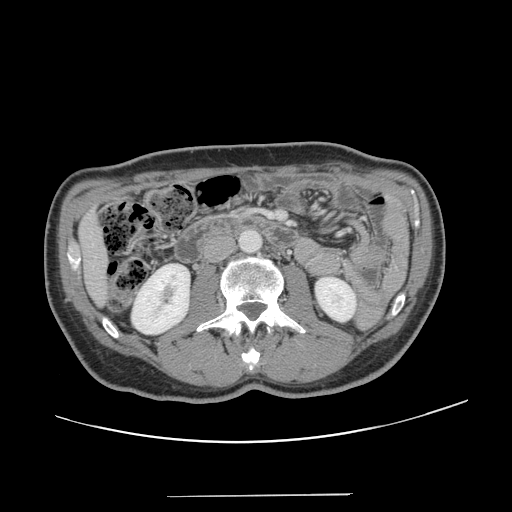
Contrast-enhanced abdominal CT, one axial slice. Slice 46 of 131 in the series (ordered by position). 120 kVp. Intravenous contrast given. Soft-tissue window (W 400 / L 40 HU). 2.5 mm slice thickness. 512 × 512 image matrix, field of view 403 × 403 mm. Male patient, age 60 years. Case-level facts recorded for this patient, not image findings: diagnosis: colorectal cancer liver metastases, imaged before liver resection; multiple liver metastases: no; largest metastasis: 2.5 cm.
Outlined on this slice (expert manual segmentation):
- liver: box from (x=81, y=214) to (x=106, y=303) px
- planned liver remnant (the part of the liver to remain after resection): (x=81, y=215)–(x=106, y=302)